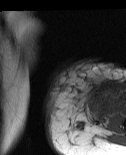
MRI of an extremity soft-tissue mass, one axial slice; MR volume resampled by the dataset authors to the PET/CT grid (not the native acquisition matrix); 3.27 mm slice thickness; 126 × 155 image matrix, field of view 123 × 151 mm. Female patient. Case-level facts recorded for this patient, not image findings: histological type: pleiomorphic leiomyosarcoma; grade: high; site of the primary tumour: left biceps.
Outlined on this slice (expert contour drawn on MRI and transferred to this co-registered scan by the dataset authors):
- gross tumour volume including surrounding oedema: bounding box <93,85,114,107> (left, top, right, bottom; pixels)